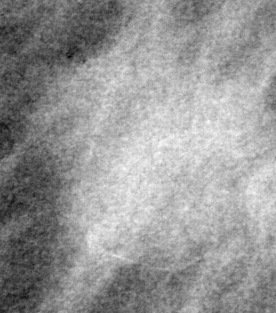
Region of interest cut from a scanned film mammogram (one marked finding), left breast, MLO view, BI-RADS breast density category 1 (scale 1–4).
Finding: mass, shape irregular, margins spiculated; BI-RADS assessment category 5; subtlety rating 4 on a 1 (subtle) to 5 (obvious) scale; pathology result (as recorded, not read from the image): malignant.